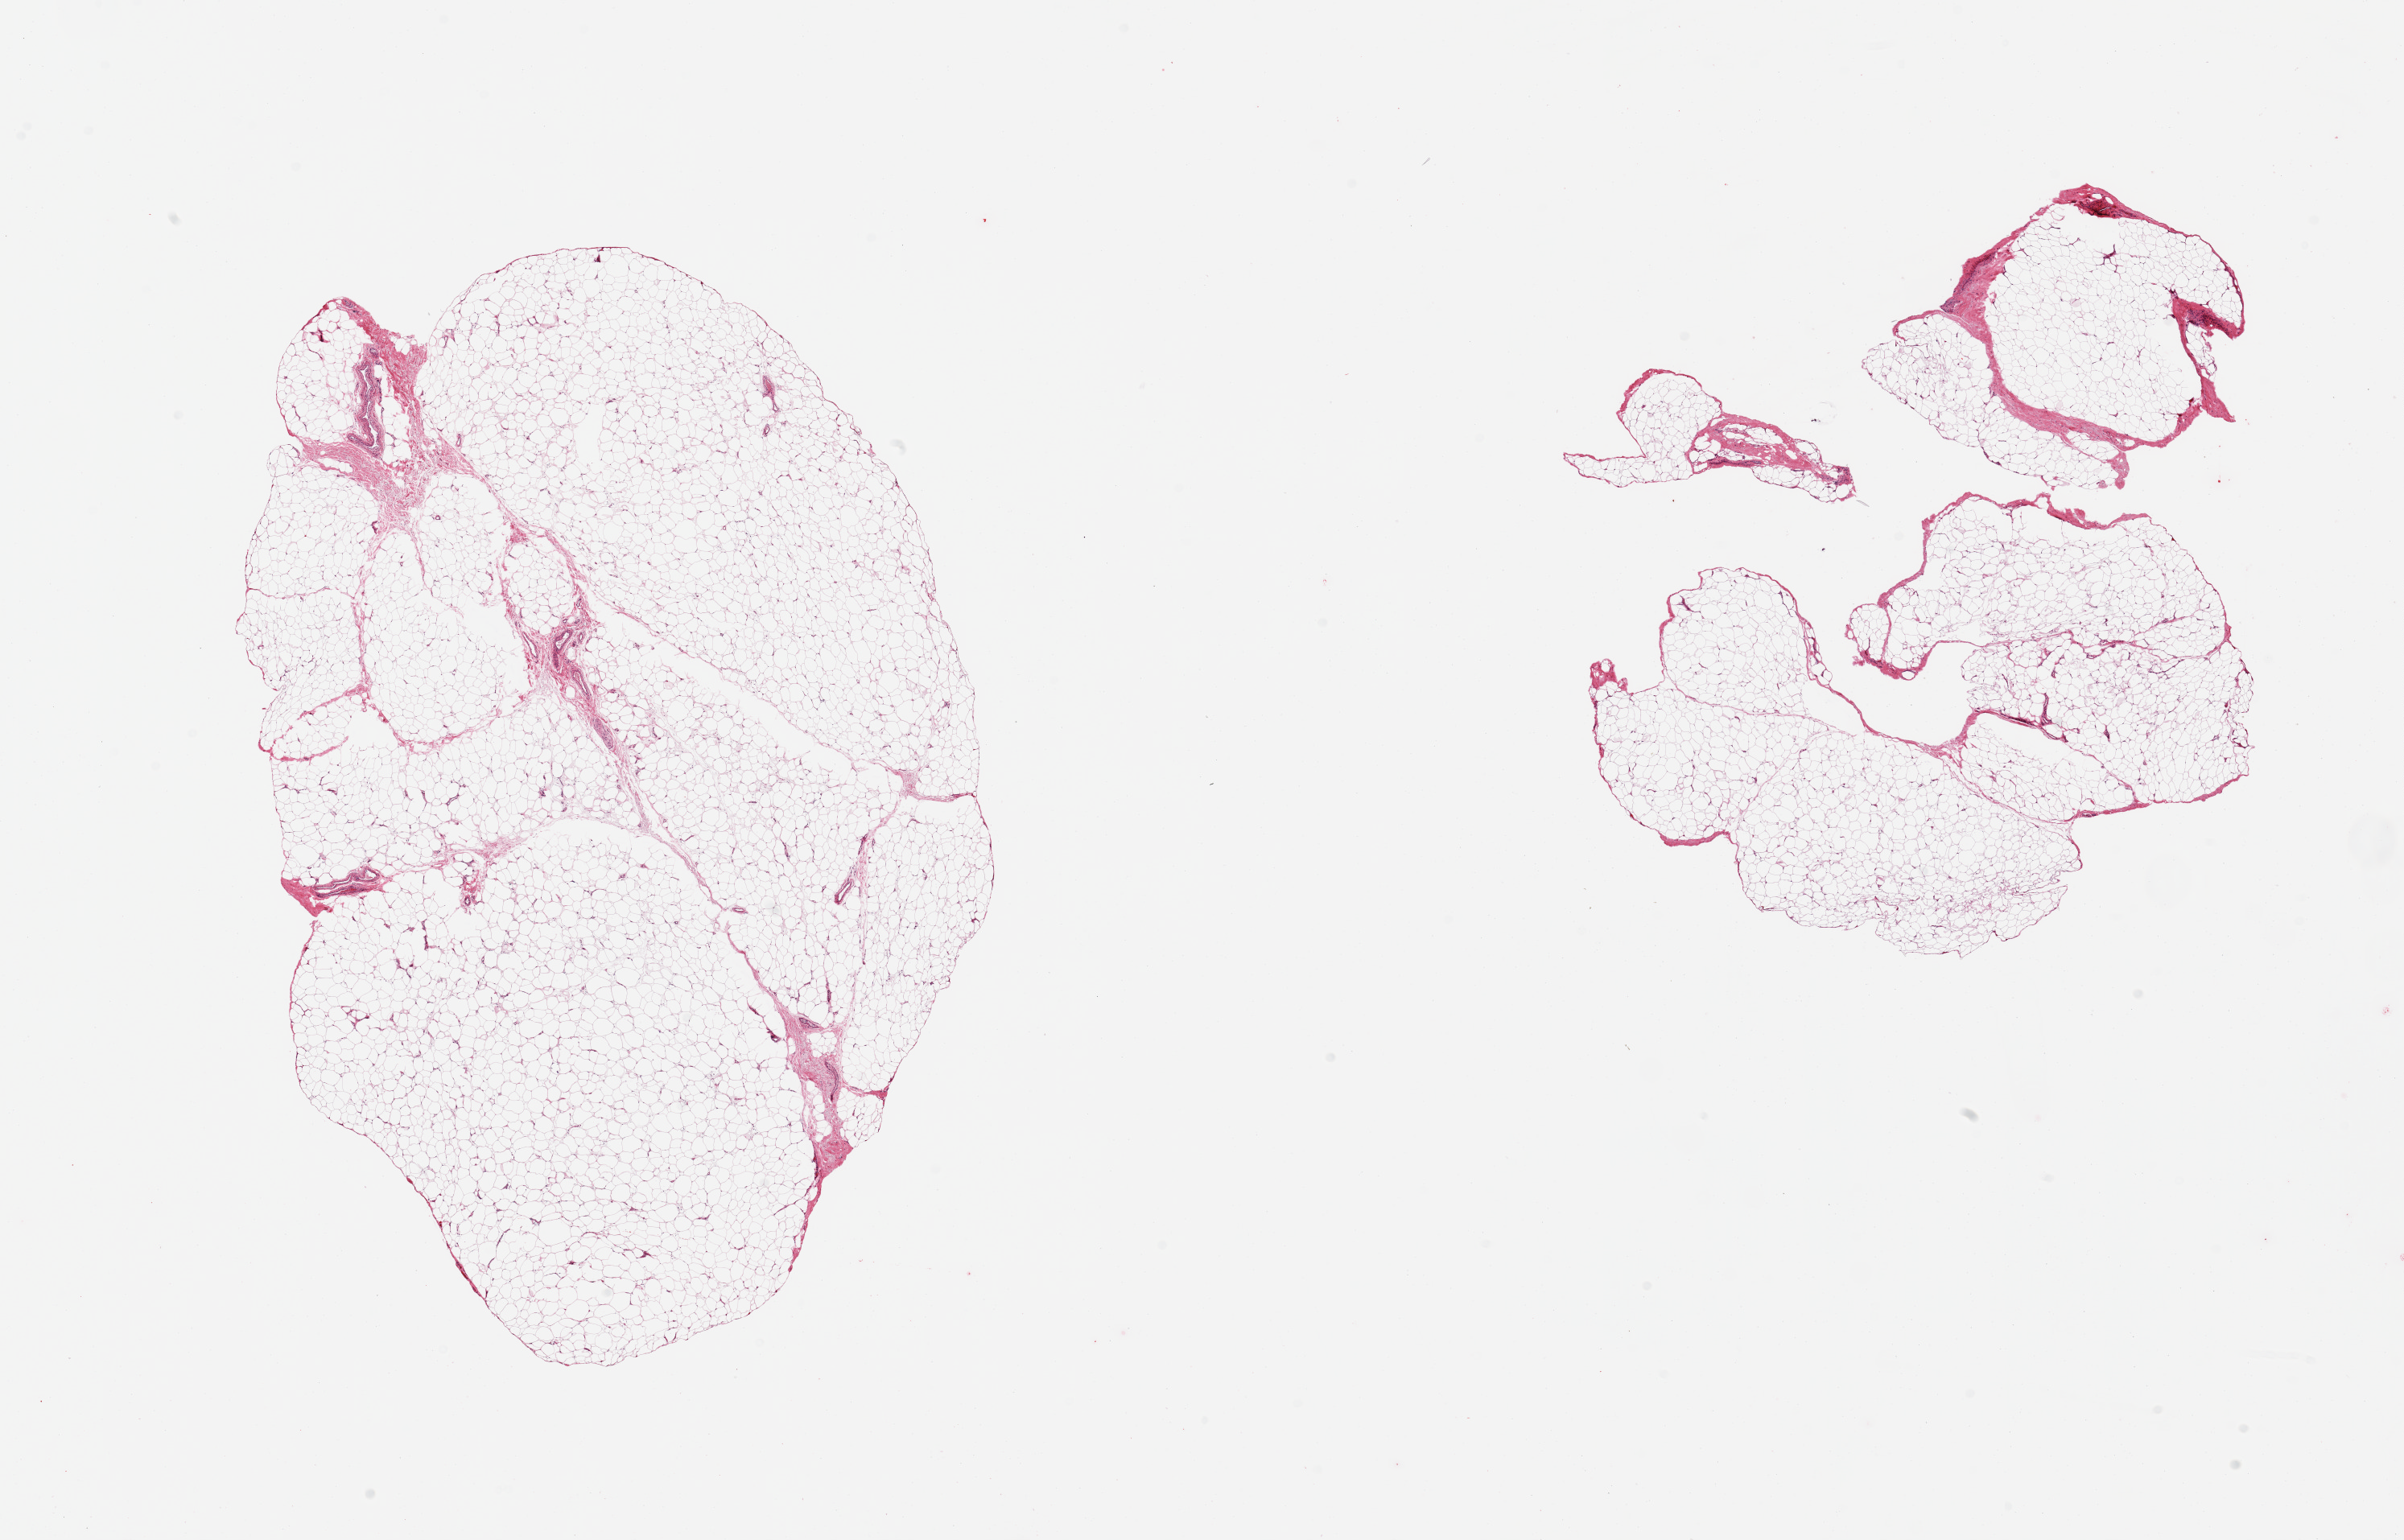
Digitized haematoxylin and eosin-stained section, brightfield, whole scanned area (about 23.6 x 15.1 mm) shown as a low-resolution overview. PAXgene-fixed paraffin-embedded (PFPE) section. Target tissue: adipose tissue. Tissue donor sample. Donor: male.
Pathologist's review note for this sample: 2 pieces, ~5-10% fascia/vascular elements.